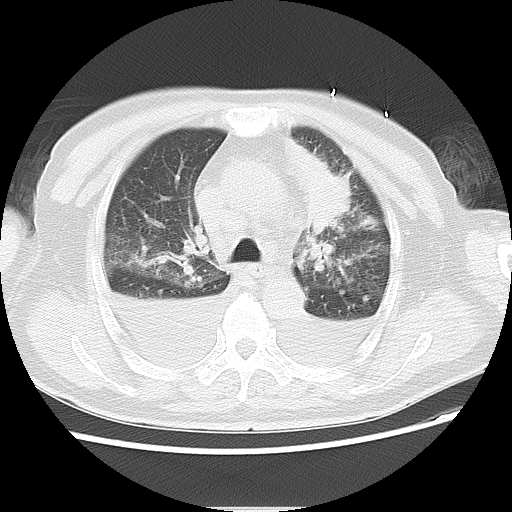
Chest CT, one axial slice; slice 17 of 22 in the series (ordered by position); reconstruction kernel LUNG; 120 kVp; lung window (W 1500 / L -600 HU); 5 mm slice thickness; 512 × 512 image matrix. Patient: male, 66 years. From the clinical record (not read from this slice): clinical TNM (as recorded): T1c N0 M0.
Structures marked on this image (bounding box drawn by a radiologist):
- lung tumour (recorded histology: adenocarcinoma): bounding box <281,135,355,230> (left, top, right, bottom; pixels)